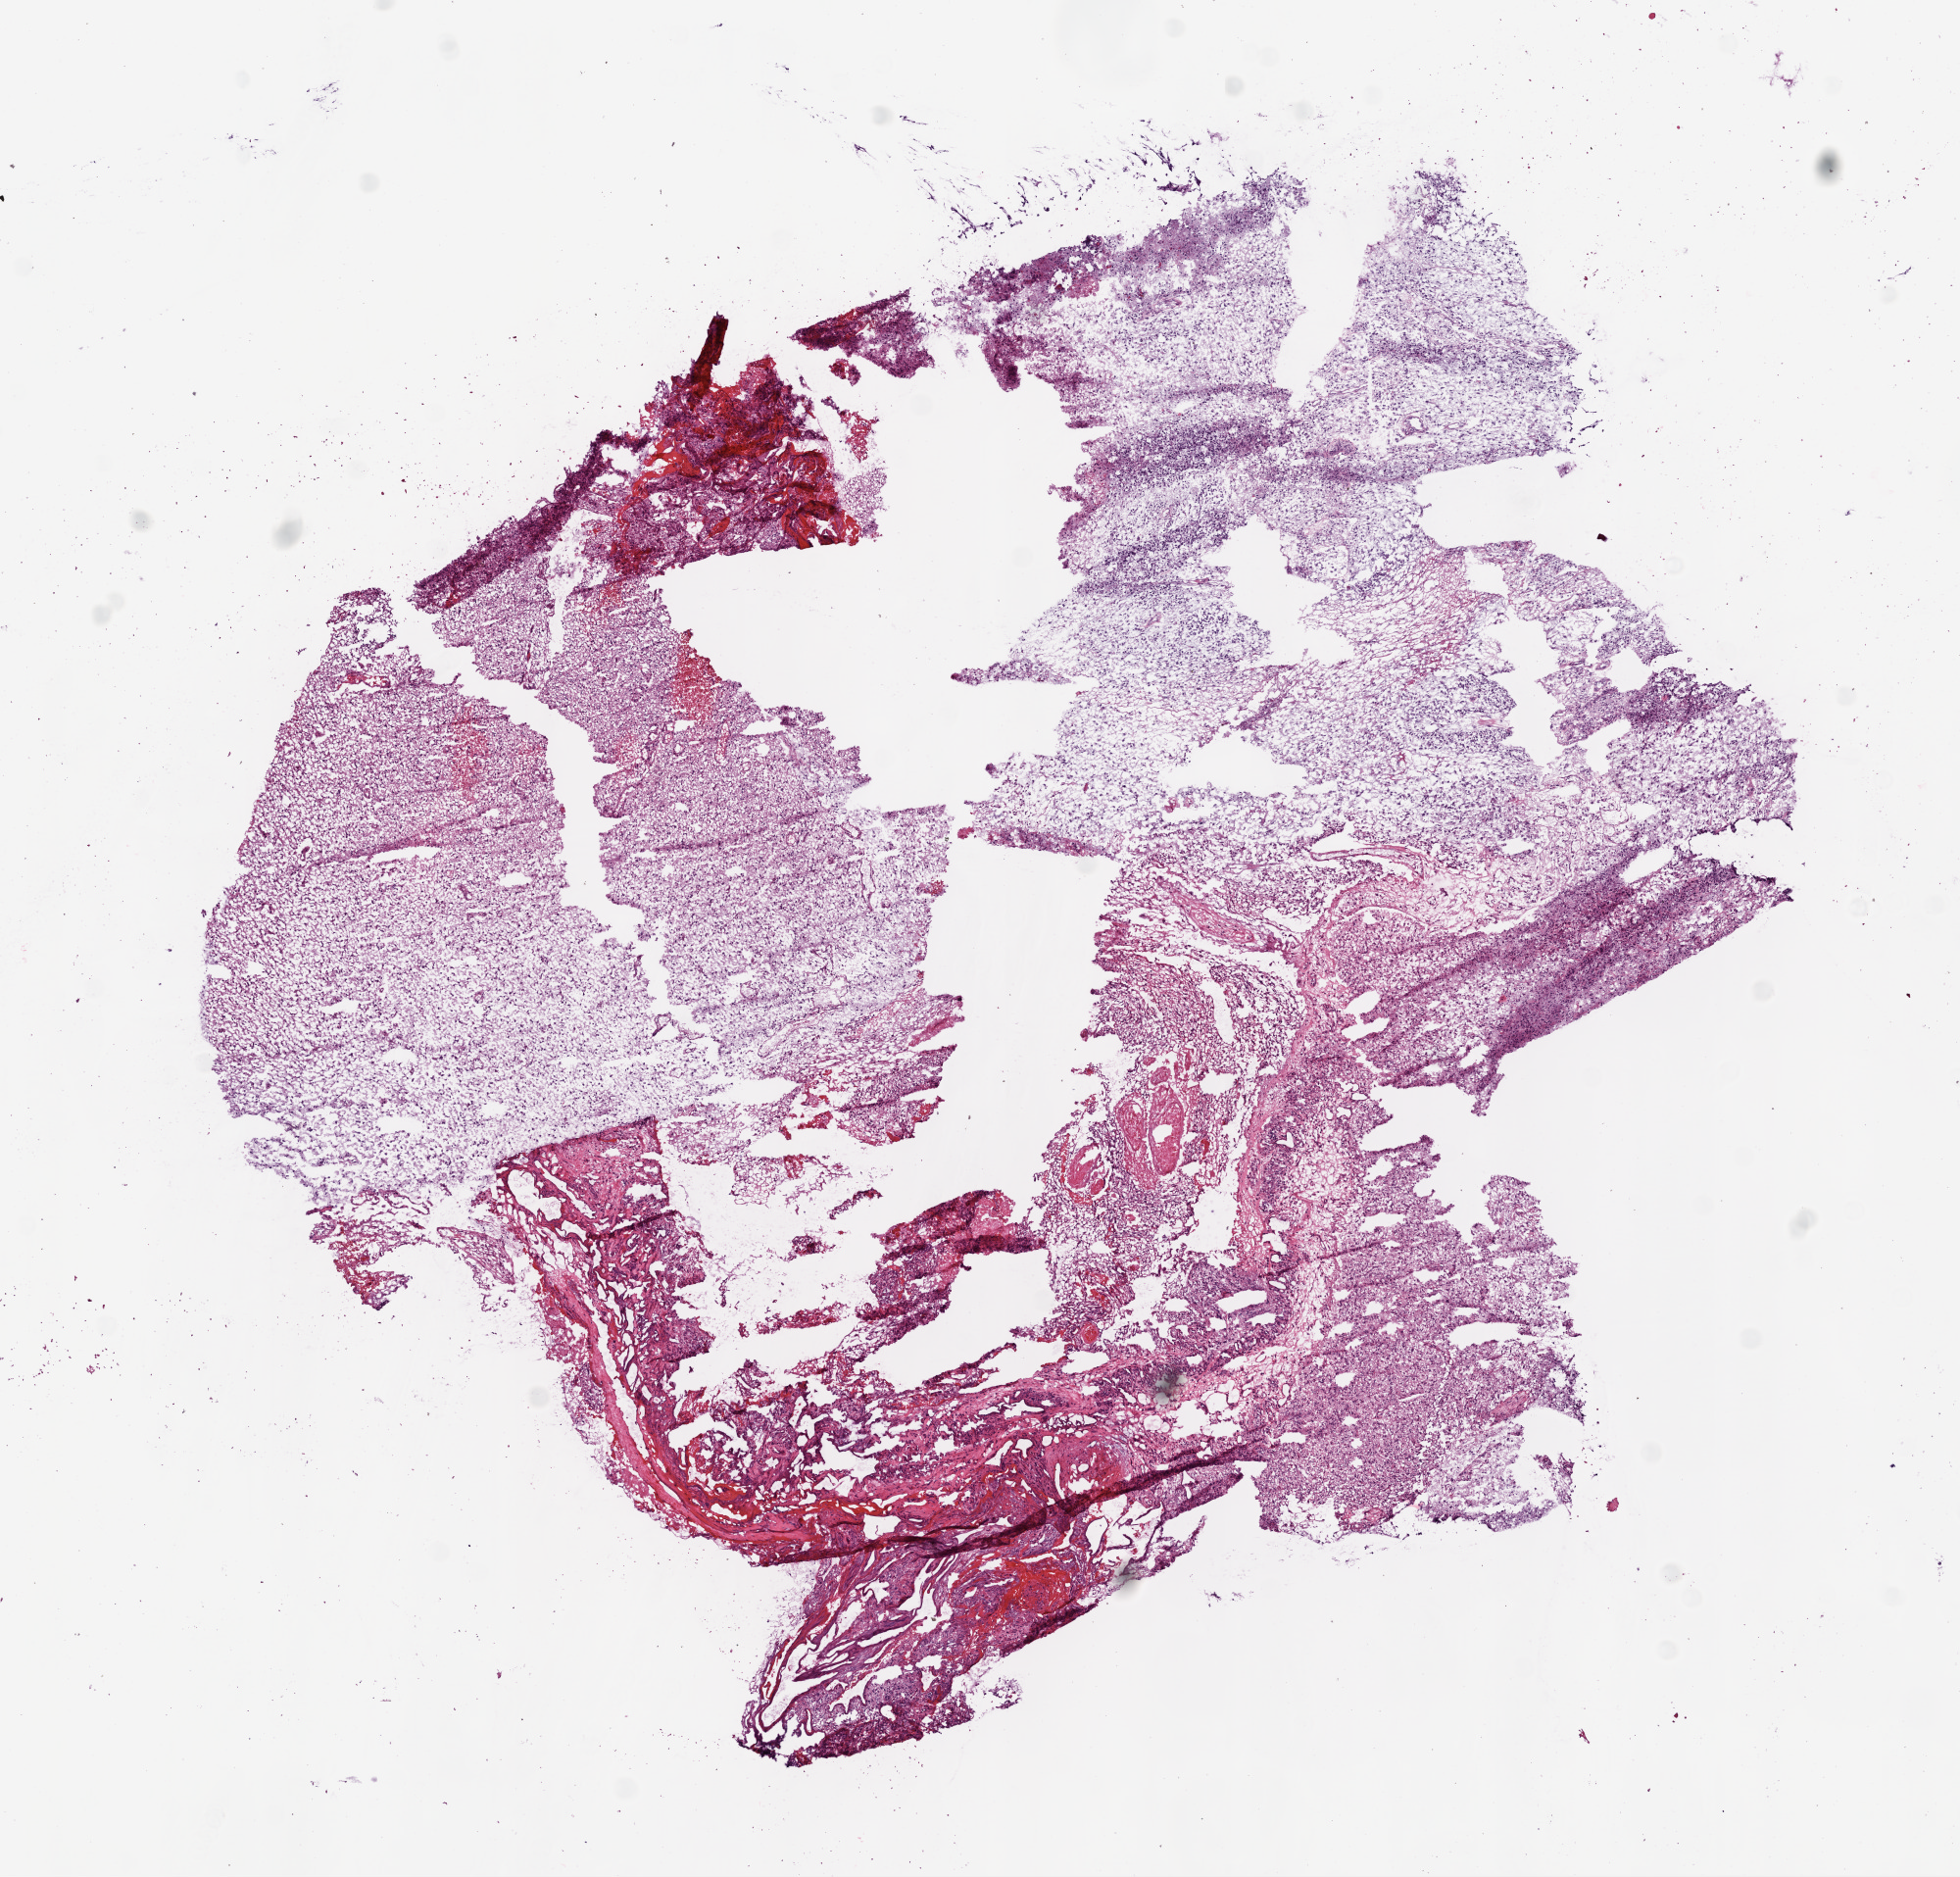
Digitized Hematoxylin and eosin (H&E) stained tissue section (whole slide), shown as a low-resolution overview of the whole scanned area (about 8.0 x 7.7 mm, slide scanned at 20x), frozen section from the top of the tissue portion, sample: primary tumour, brain. Male, age 67 years at initial diagnosis. Pathologist review of this section (percent, as recorded): tumour cells 82%, tumour nuclei 80%, normal cells 0%, stromal cells 15%, necrosis 10%.
Pathologic diagnosis: Glioblastoma.